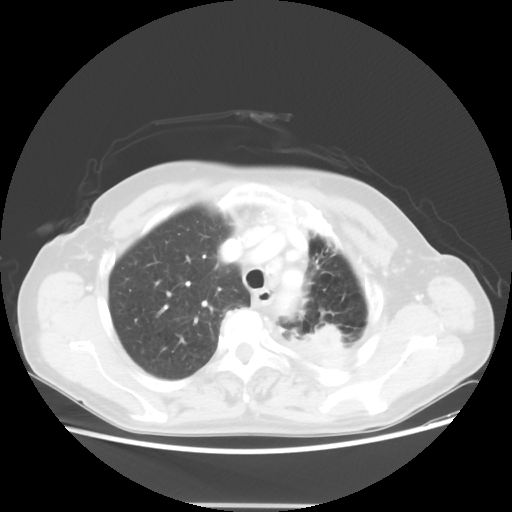
Chest CT, one axial slice. Slice 42 of 56 in the series (ordered by position). Reconstruction kernel STANDARD. Lung window (W 1500 / L -600 HU). 5 mm slice thickness. 512 × 512 image matrix, field of view 377 × 377 mm. Female patient, age 63 years. From the clinical record (not read from this slice): clinical TNM (as recorded): T2a N0 M0.
Structures marked on this image (rectangle marked by the reading radiologist):
- lung tumour (recorded histology: adenocarcinoma): bounding box [x1, y1, x2, y2] px = [298, 315, 346, 369]